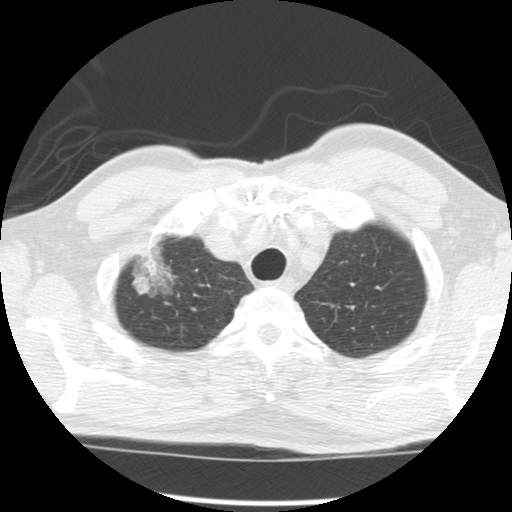
Axial slice from a low-dose chest CT screening exam; second screening round (one year after baseline); lung window (W 1500 / L -600 HU); standard (soft-tissue) reconstruction kernel (STANDARD); 120 kVp; slice 16 of 120 in the series. Male participant, aged 64 years at enrolment. Former smoker at enrolment.
- Expert-annotated lung lesion, box from (x=122, y=237) to (x=187, y=306) px.
- The screening reader recorded 2 non-calcified nodules or masses ≥4 mm on this exam (right upper lobe, left upper lobe); which of them this box marks is not recorded.
- Later outcome: lung cancer diagnosed 429 days after this screen — adenocarcinoma, NOS, right upper lobe, well differentiated (G1), stage IB (AJCC 6th edition), 45 mm at pathology.